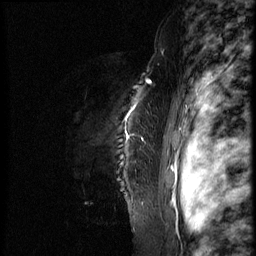
Breast MRI (dynamic contrast-enhanced), one sagittal slice. Position 60 of 66 along the scan axis. Dynamic contrast-enhanced series, image 2 of 3 at this slice position (ordered by acquisition). 1.5 T. TE 4.2 ms, TR 8.9 ms. 256 × 256 image matrix, field of view 200 × 200 mm. Female patient, age 39 years. Case-level facts recorded for this patient, not image findings: setting: breast cancer imaged before/during neoadjuvant chemotherapy; receptor status: HER2-positive.
Annotated regions visible in this slice (semi-automatic segmentation, software-assisted and operator-edited):
- analysis volume of interest (the breast-tissue region the enhancement analysis was run in; not a lesion): box from (x=74, y=75) to (x=159, y=218) px
- tumour enhancement mask (voxels above the 140 % enhancement threshold inside the analysis volume of interest): (x=149, y=82)–(x=152, y=85)